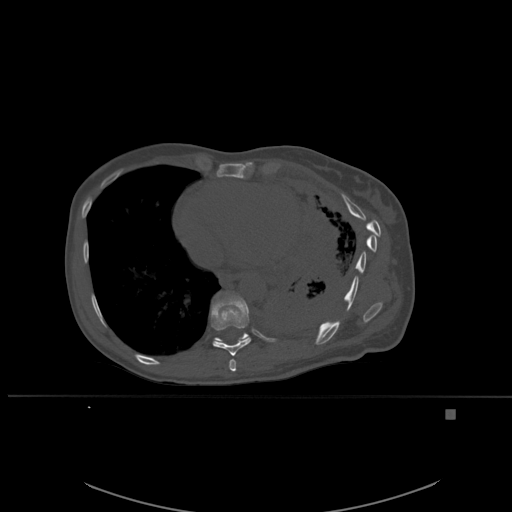
CT including the spine, one axial slice; position 331 of 537 along the scan axis; bone window (W 1800 / L 400 HU); 1.5 mm slice thickness; 512 × 512 image matrix, field of view 440 × 440 mm. Patient: female, 45 years. Case-level facts recorded for this patient, not image findings: primary cancer: lung.
Annotated regions visible in this slice (semi-automatically segmented with operator editing):
- T10 vertebra: bounding box <213,292,249,344> (left, top, right, bottom; pixels)
- T8 vertebra: <229,359,237,372>
- T9 vertebra: <210,292,251,356>